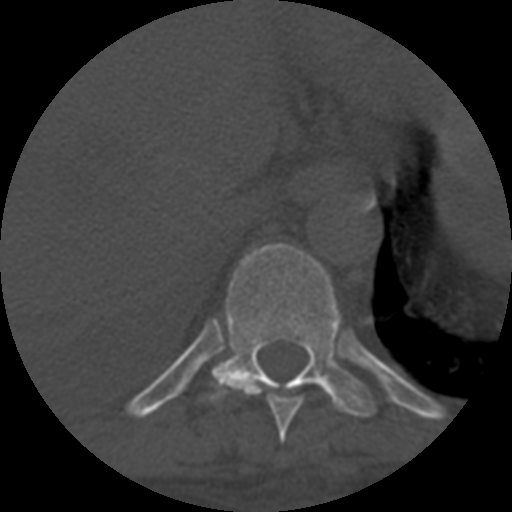
CT including the spine, one axial slice; slice 364 of 708 in the series (ordered by position); one of 3 acquisitions stored at this slice position; bone window (W 1800 / L 400 HU); 1.25 mm slice thickness; 512 × 512 image matrix, field of view 160 × 160 mm. Patient age 55 years. From the clinical record (not read from this slice): primary cancer: colon.
Outlined on this slice (semi-automatic segmentation, software-assisted and operator-edited):
- T10 vertebra: bounding box <208,243,377,418> (left, top, right, bottom; pixels)
- T9 vertebra: <220,378,303,443>